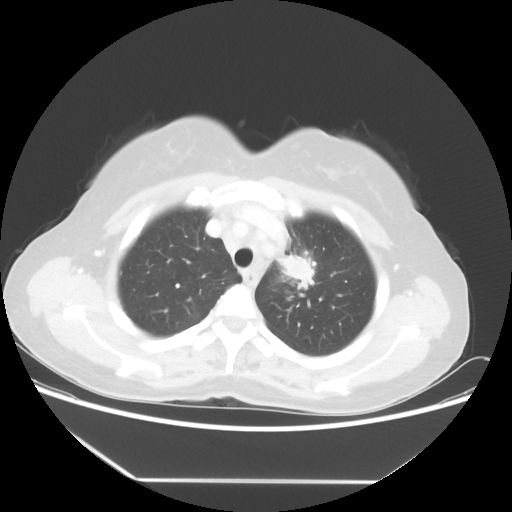
Chest CT, one axial slice; reconstruction kernel STANDARD; 100 kVp; lung window (W 1500 / L -600 HU); 5 mm slice thickness; 512 × 512 image matrix. Female patient, age 50 years. From the clinical record (not read from this slice): clinical TNM (as recorded): T2 N3 M0.
Annotated regions visible in this slice (rectangle marked by the reading radiologist):
- lung tumour (recorded histology: adenocarcinoma): bounding box <269,242,326,303> (left, top, right, bottom; pixels)